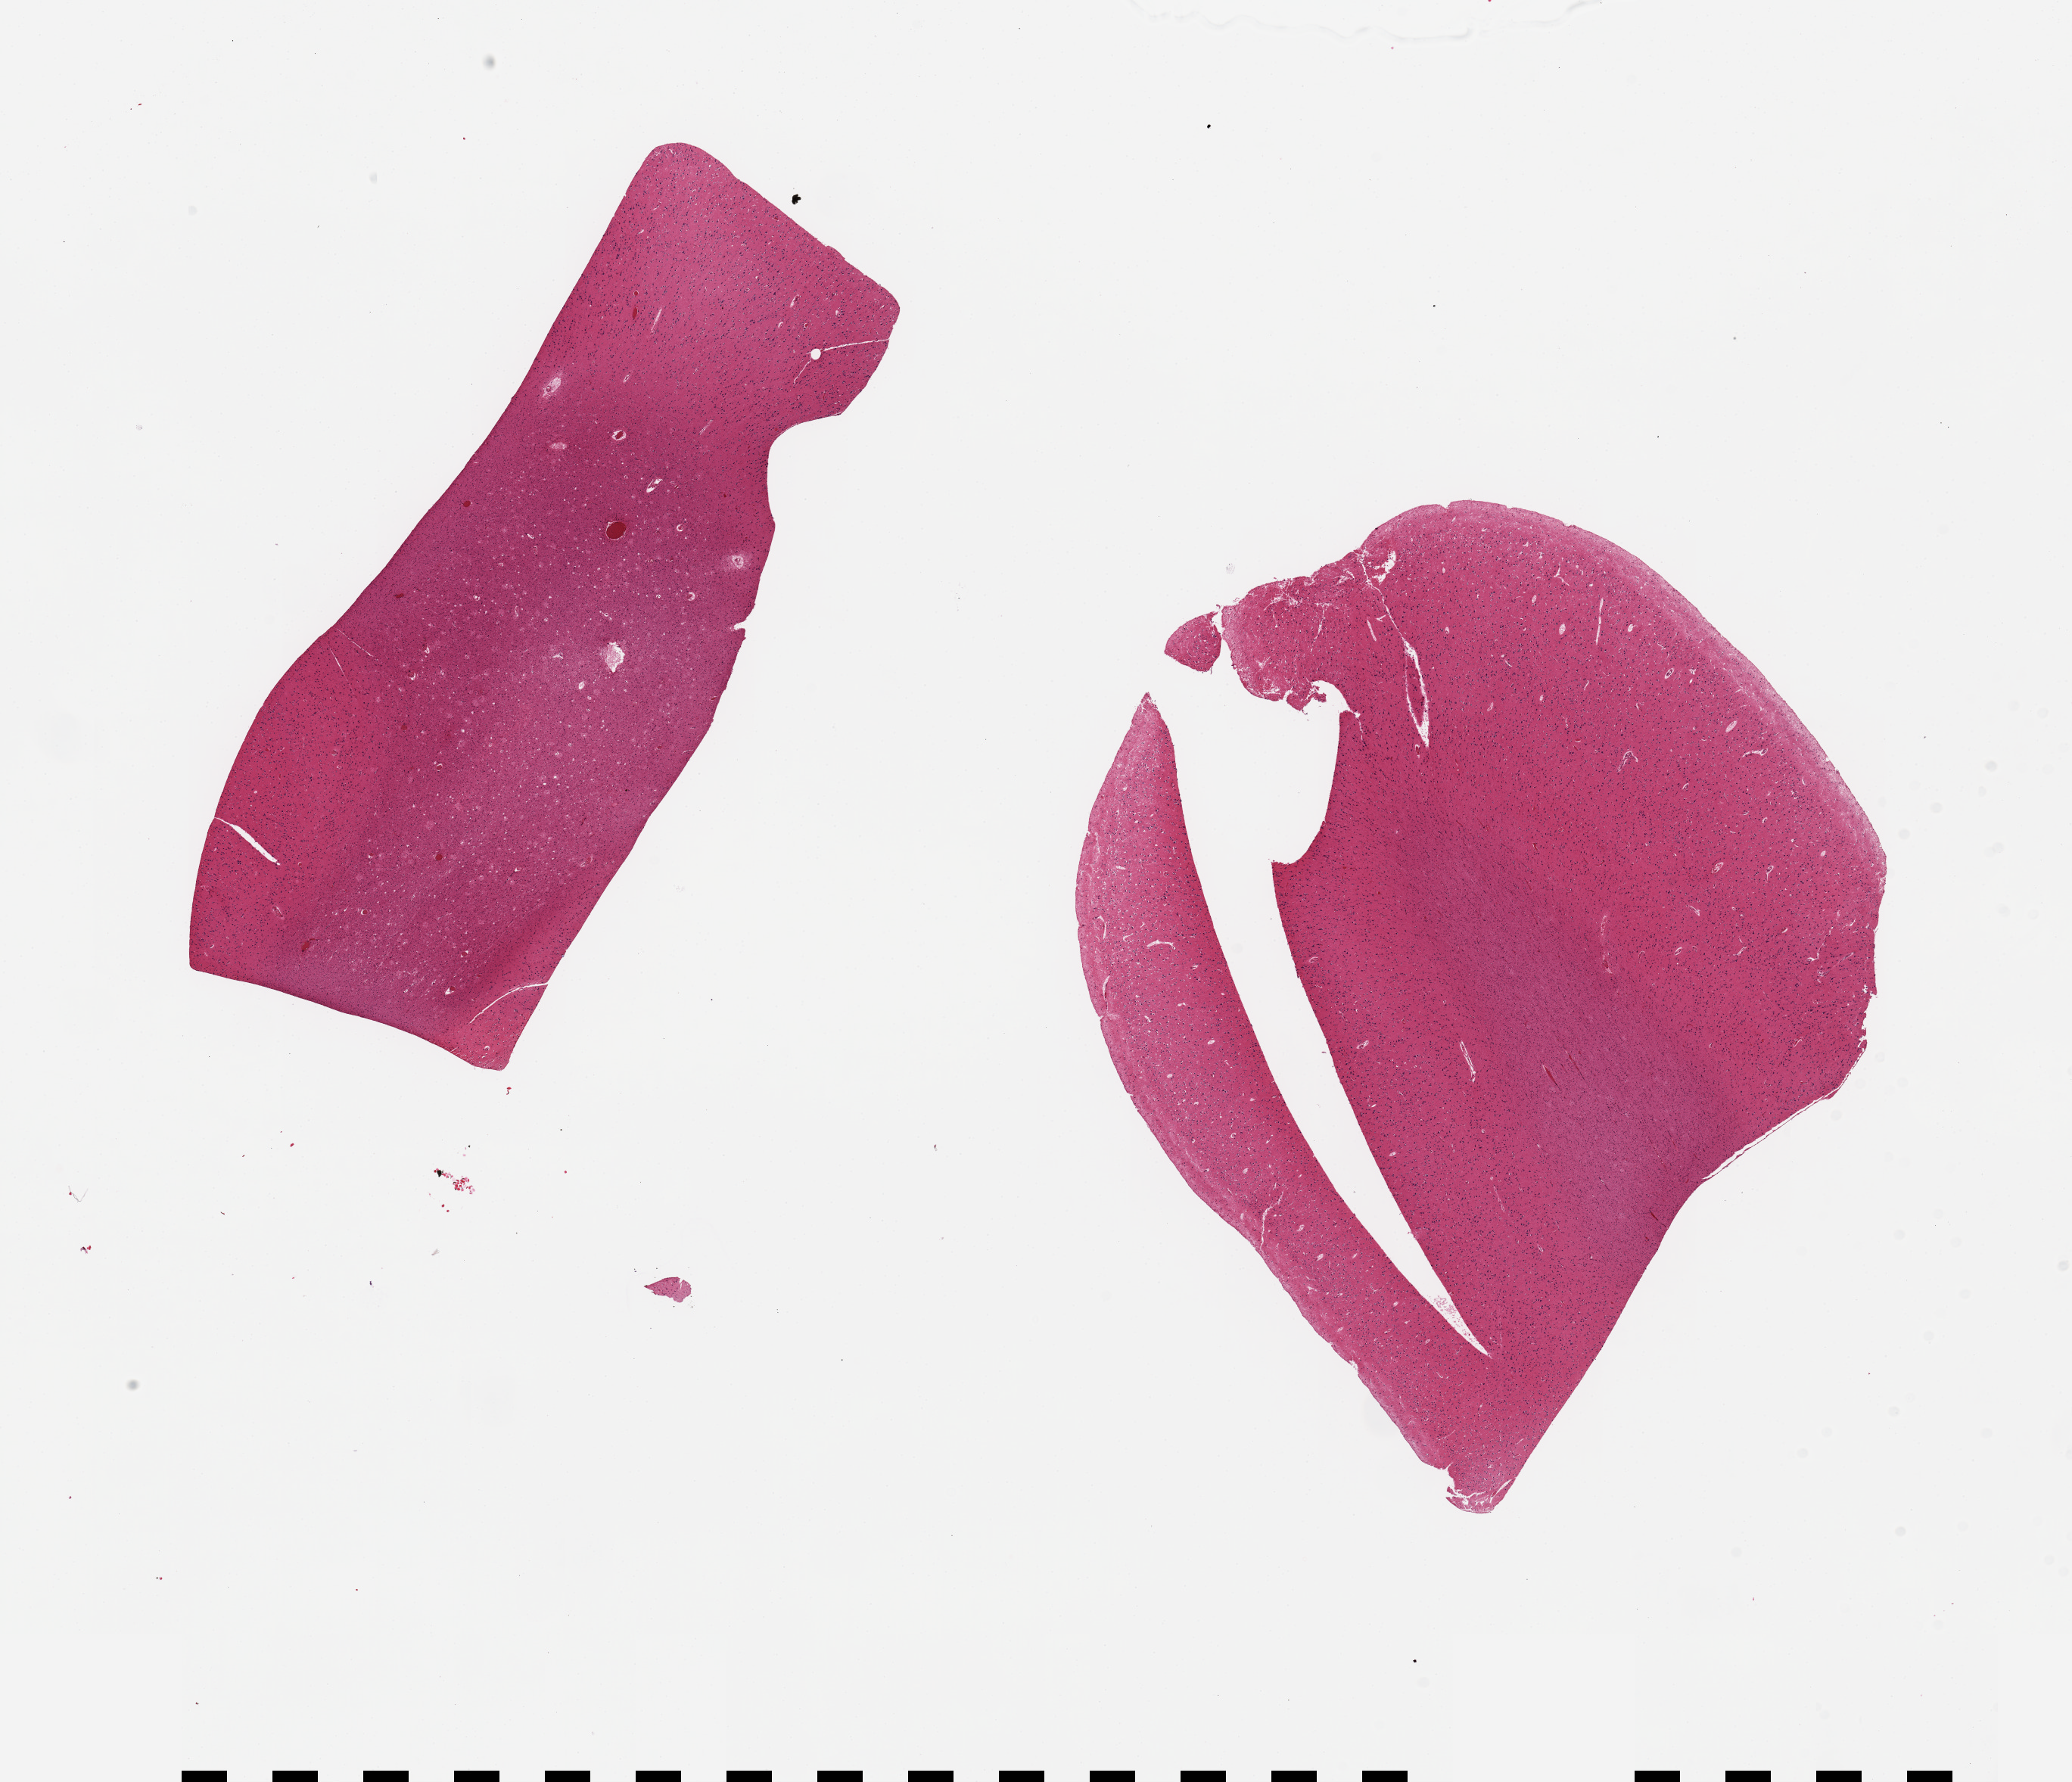
Digitized hematoxylin and eosin (H&E)-stained section — shown as a low-resolution overview of the whole scanned area (about 21.7 x 18.6 mm, from a 20x scan); PAXgene-fixed, paraffin-embedded tissue; section of cerebral cortex (target tissue); tissue donor sample. Donor sex: male.
Review note (as recorded): 2 pieces.